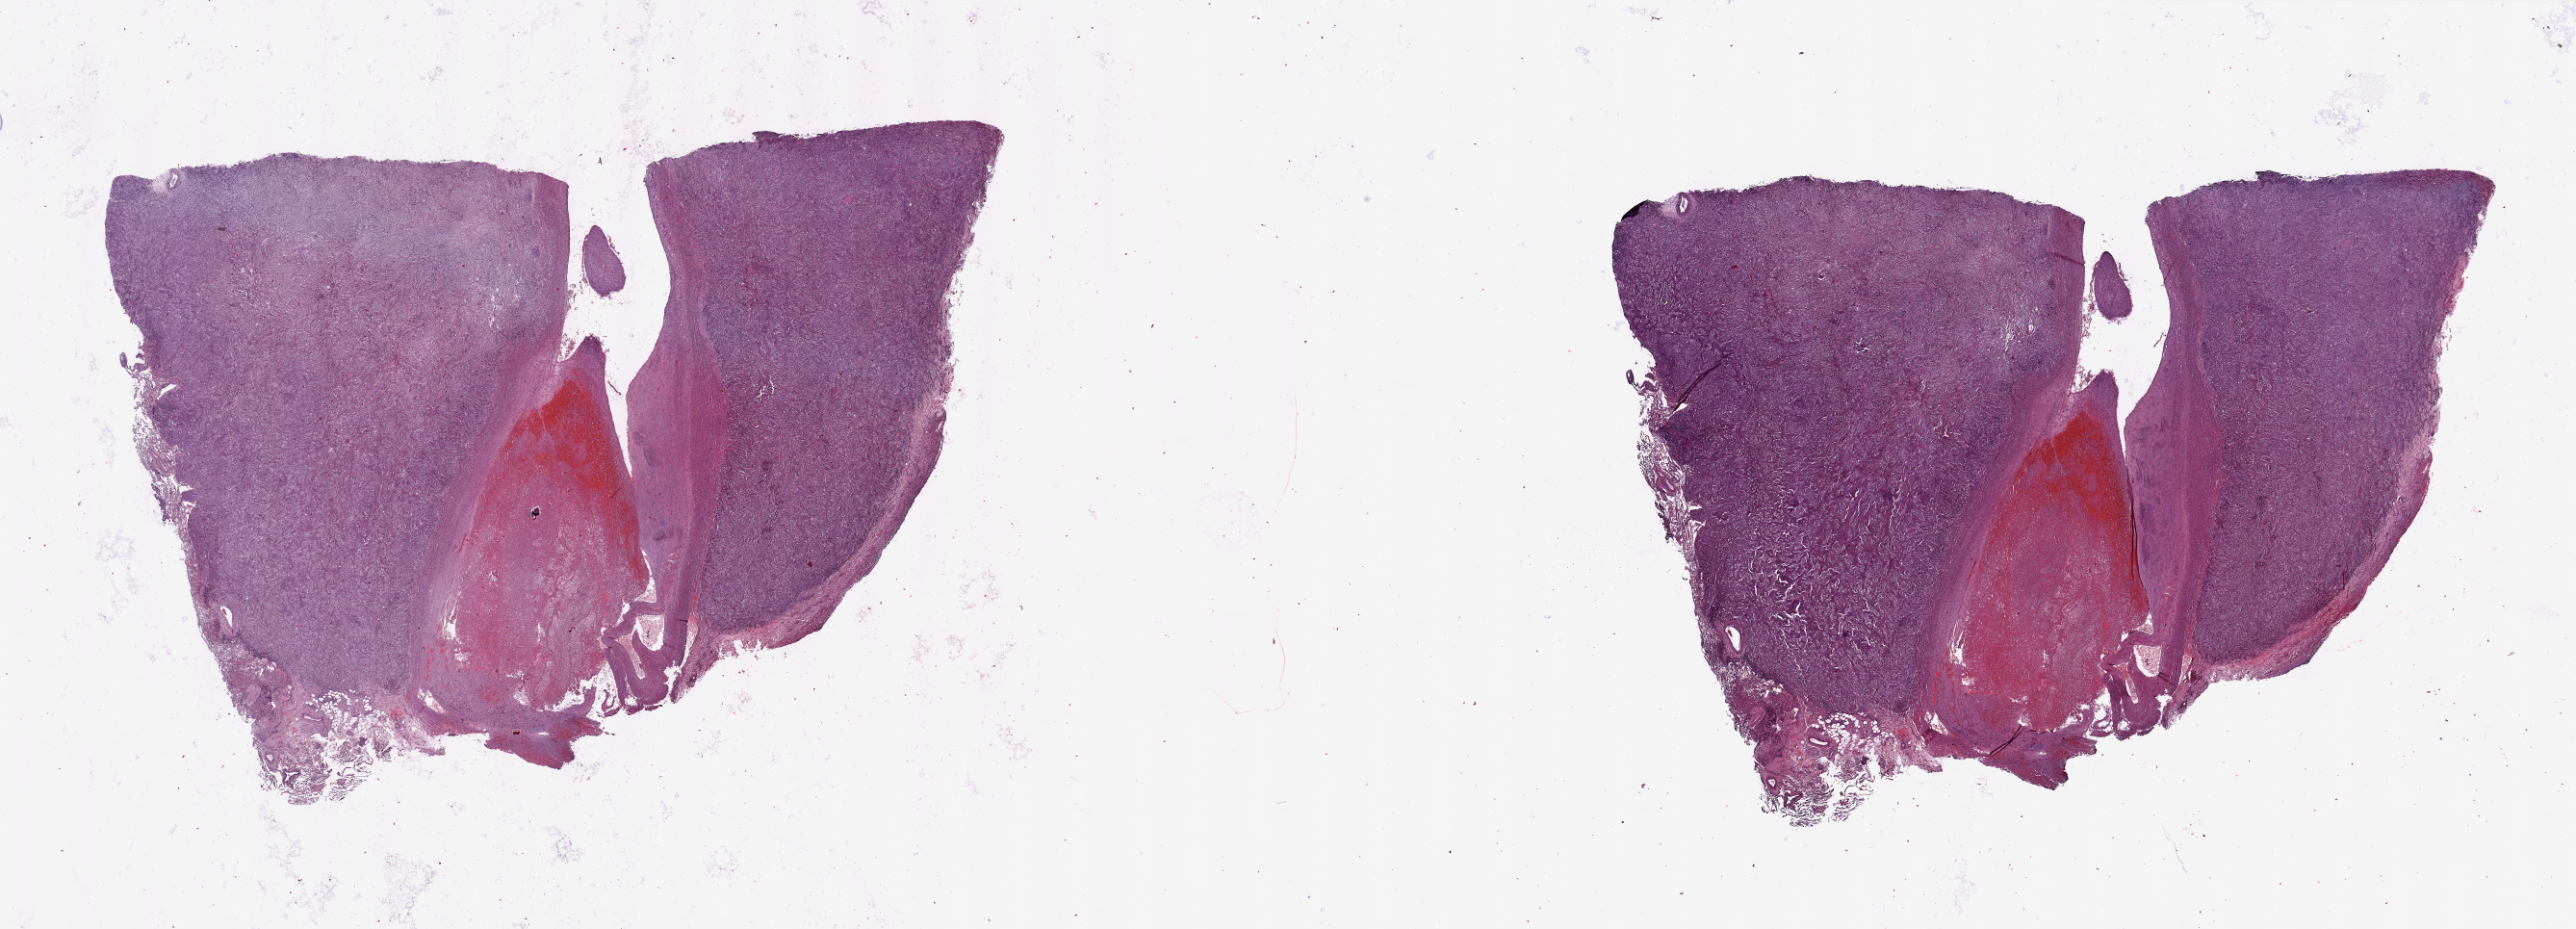
Whole-slide histology image, Hematoxylin and eosin (H&E) stained, a low-resolution overview of the entire scanned area, about 42.3 x 15.3 mm; tumour tissue sample, lung. 72-year-old male patient. Histologic grade: G3 (poorly differentiated).
• primary tumour site (as recorded): left upper lobe
• AJCC pathologic stage: IB
• diagnosis: Adenocarcinoma, NOS